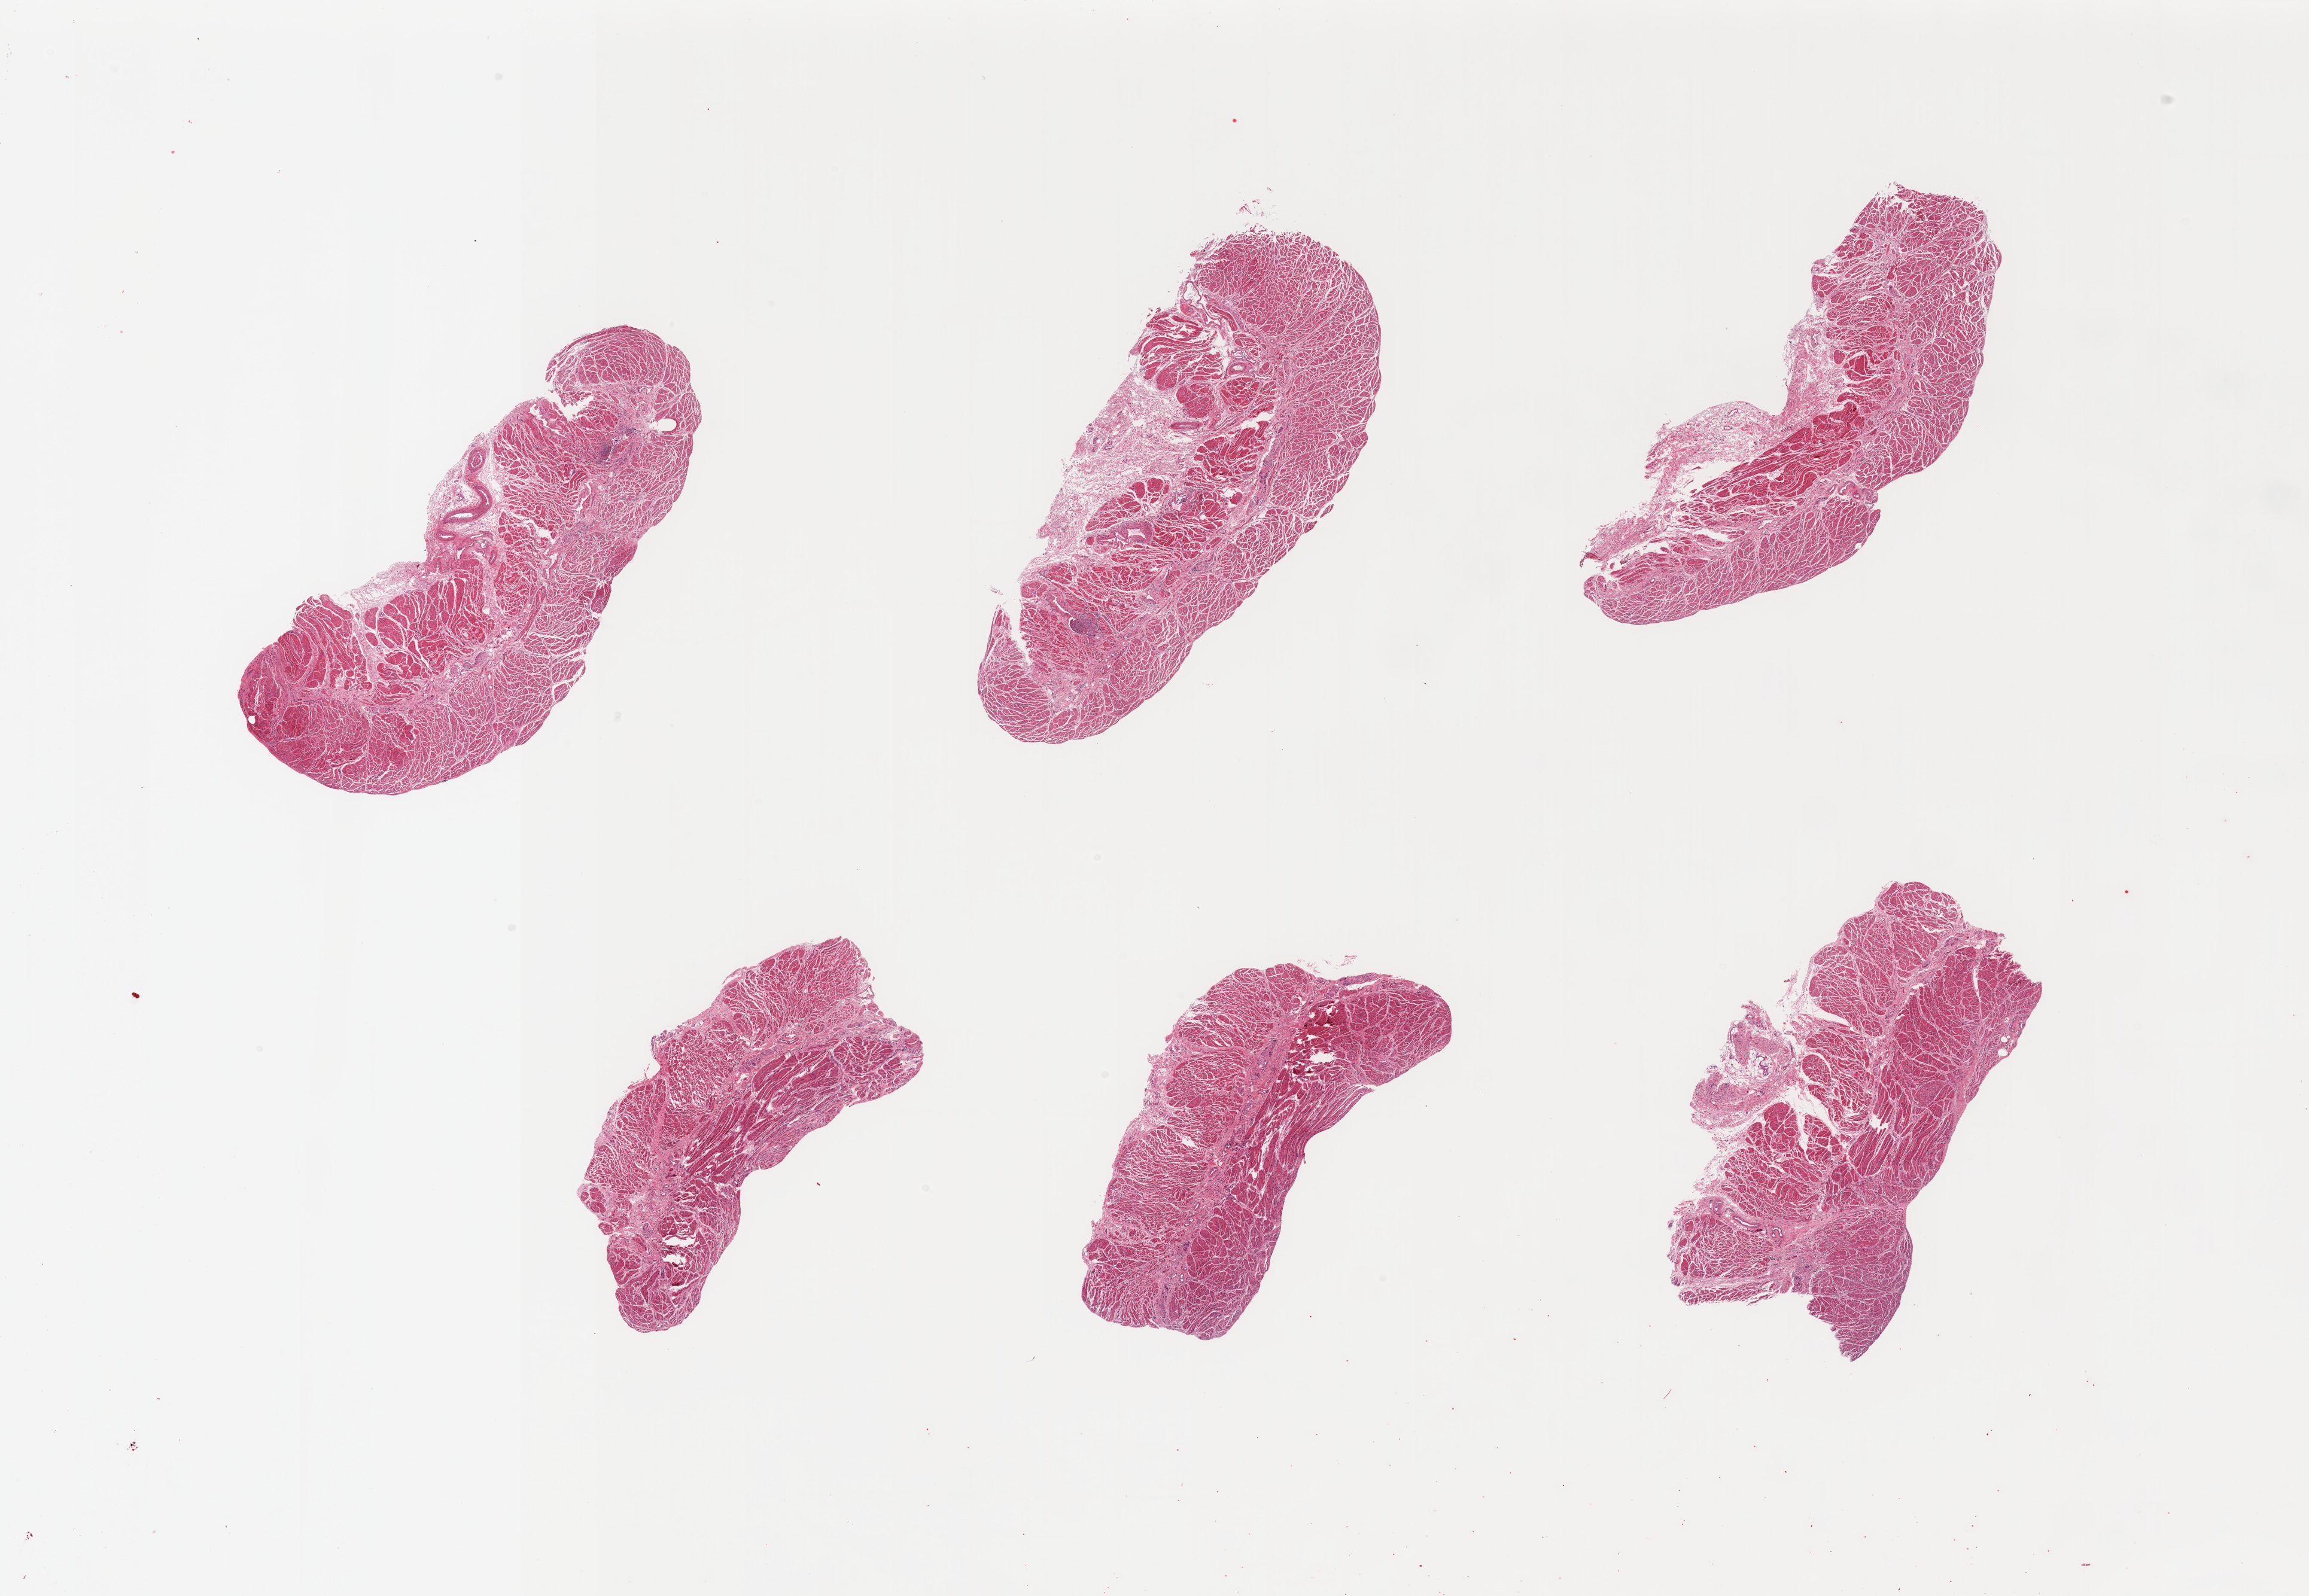
Digitized H&E-stained section — whole scanned area (about 30.5 x 21.1 mm, acquisition: 20x scan) shown as a low-resolution overview, PAXgene-fixed, paraffin-embedded tissue, sampled site (target tissue): gastroesophageal junction, donor tissue sample.
Reviewer comment on this tissue sample: 6 pieces; submucosal fibrous stroma comprises 10% of 3 pieces.